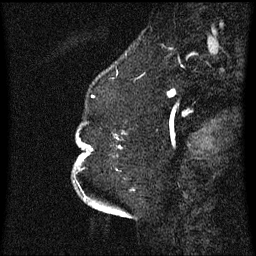
Breast MRI (dynamic contrast-enhanced), one sagittal slice. Slice 17 of 60 in the series (ordered by position). Dynamic contrast-enhanced series, image 2 of 3 at this slice position (ordered by acquisition). 1.5 T. TE 4.2 ms, TR 8.4 ms. 2.3 mm slice thickness. 256 × 256 image matrix. Female patient, age 52 years. From the clinical record (not read from this slice): setting: breast cancer imaged before/during neoadjuvant chemotherapy; receptor status: HR-positive, HER2-negative.
Outlined on this slice (semi-automatic segmentation, software-assisted and operator-edited):
- analysis volume of interest (the breast-tissue region the enhancement analysis was run in; not a lesion): bounding box (x1, y1, x2, y2) in pixels: (75, 122, 125, 181)
- tumour enhancement mask (voxels above the 70 % enhancement threshold inside the analysis volume of interest): (91, 138, 117, 151)